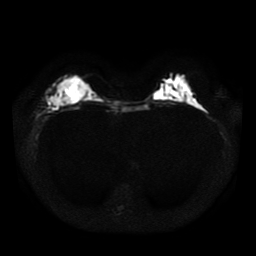
Breast MRI, one axial slice. Position 14 of 41 along the scan axis. Diffusion-weighted series; image 2 of 4 stored at this slice position (different b-values; order by instance number). 1.5 T. 5 mm slice thickness. 256 × 256 image matrix, field of view 330 × 330 mm. Female patient.
Outlined on this slice (outlined manually by an expert reader):
- tumour on diffusion-weighted imaging: bounding box <49,95,69,107> (left, top, right, bottom; pixels)